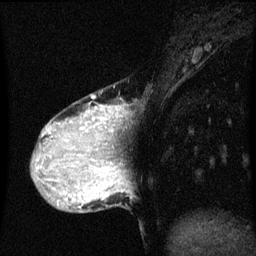
Breast MRI (dynamic contrast-enhanced), one sagittal slice; position 16 of 60 along the scan axis; dynamic contrast-enhanced series, image 2 of 3 at this slice position (ordered by acquisition); 1.5 T; TE 4.2 ms, TR 8 ms; 256 × 256 image matrix. Patient: female, 36 years.
Structures marked on this image (semi-automatically segmented with operator editing):
- analysis volume of interest (the breast-tissue region the enhancement analysis was run in; not a lesion): bounding box (x1, y1, x2, y2) in pixels: (33, 90, 123, 169)
- tumour enhancement mask (voxels above the 70 % enhancement threshold inside the analysis volume of interest): (43, 106, 121, 169)